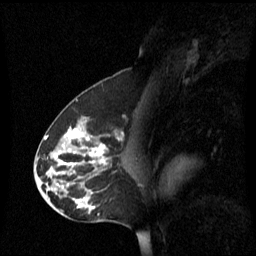
Breast MRI (dynamic contrast-enhanced), one sagittal slice; slice 34 of 60 in the series (ordered by position); dynamic contrast-enhanced series, image 2 of 3 at this slice position (ordered by acquisition); 1.5 T; TE 4.2 ms, TR 8.4 ms; 2.2 mm slice thickness; 256 × 256 image matrix, field of view 240 × 240 mm. Patient: female, 45 years. From the clinical record (not read from this slice): setting: breast cancer imaged before/during neoadjuvant chemotherapy; receptor status: HR-positive, HER2-negative.
Outlined on this slice (semi-automatic segmentation, software-assisted and operator-edited):
- analysis volume of interest (the breast-tissue region the enhancement analysis was run in; not a lesion): bounding box (x1, y1, x2, y2) in pixels: (38, 120, 133, 221)
- tumour enhancement mask (voxels above the 70 % enhancement threshold inside the analysis volume of interest): (54, 124, 105, 207)